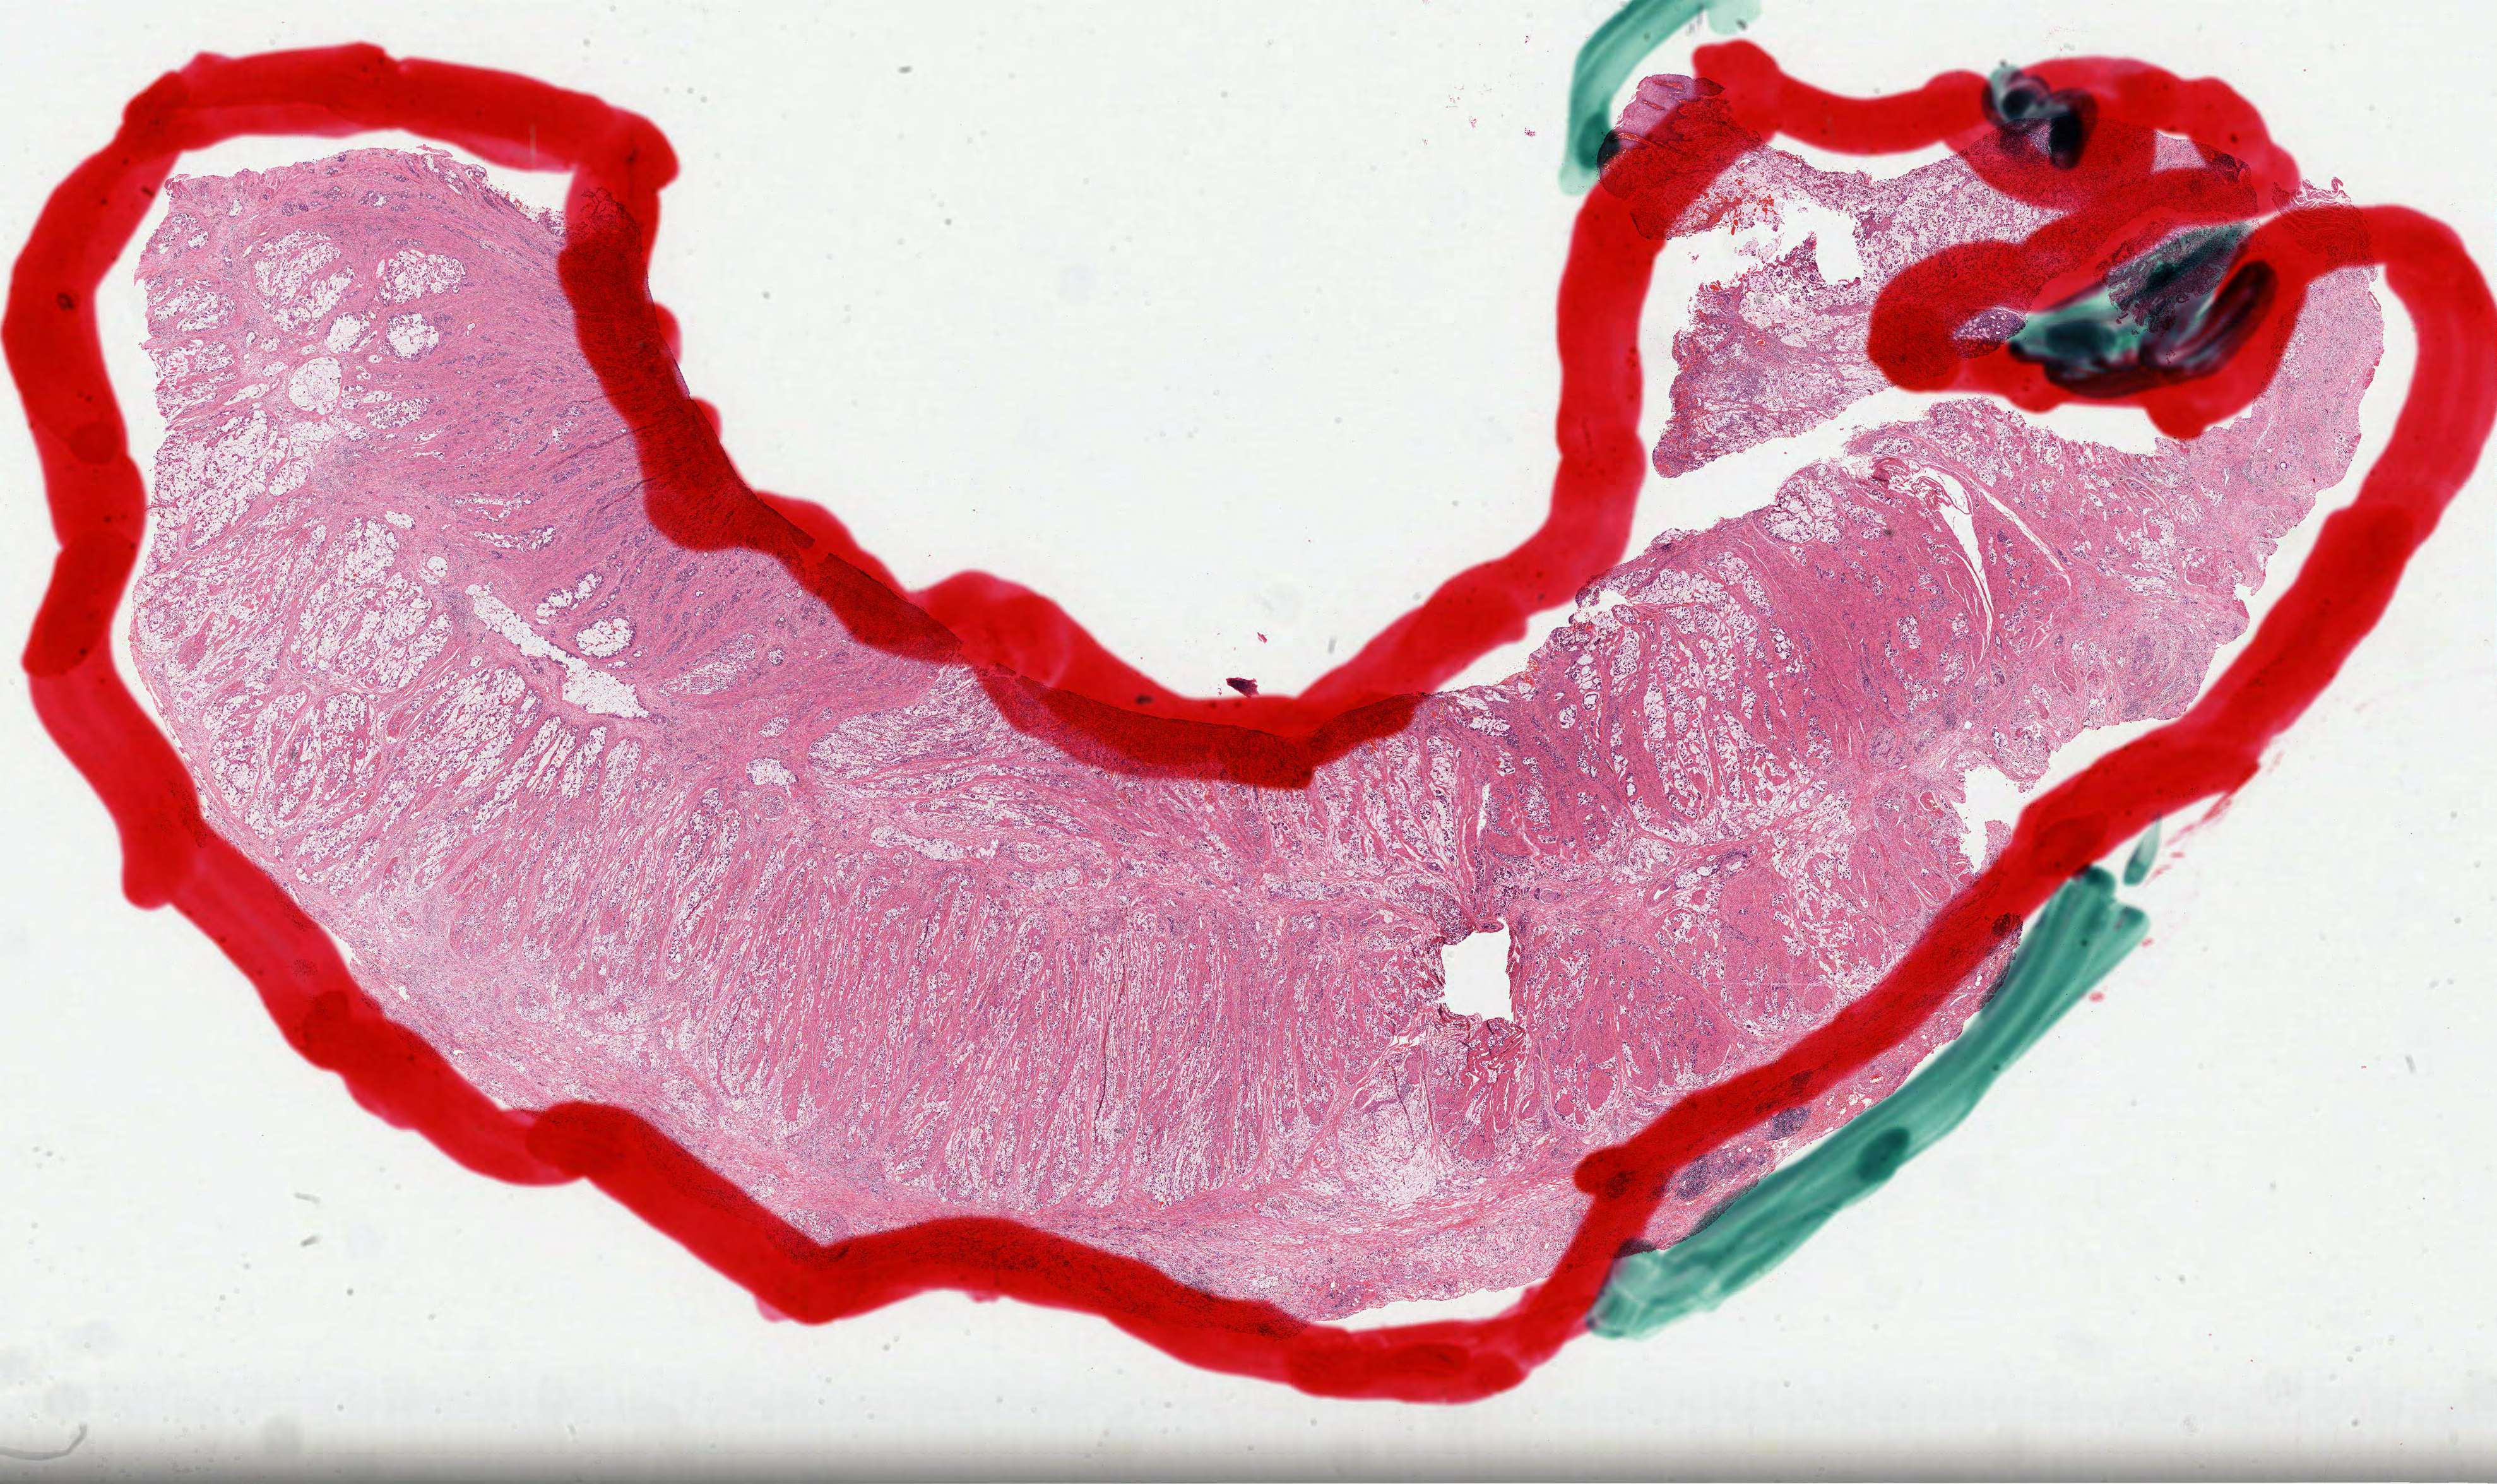
Hematoxylin and eosin (H&E) stained whole-slide image, low-resolution overview of the scanned area, about 31.9 x 19.0 mm (slide scanned at 40x), formalin-fixed paraffin-embedded (FFPE) diagnostic section, primary tumour sample from the stomach. Male patient; age at initial diagnosis 59 years. Histologic grade: G3 (poorly differentiated).
- diagnosis: Mucinous adenocarcinoma (cardia, NOS)
- AJCC pathologic stage: IIIA (7th edition)
- TNM: T4a N1 M0
- lymph nodes positive (case pathology): 1 of 7 examined